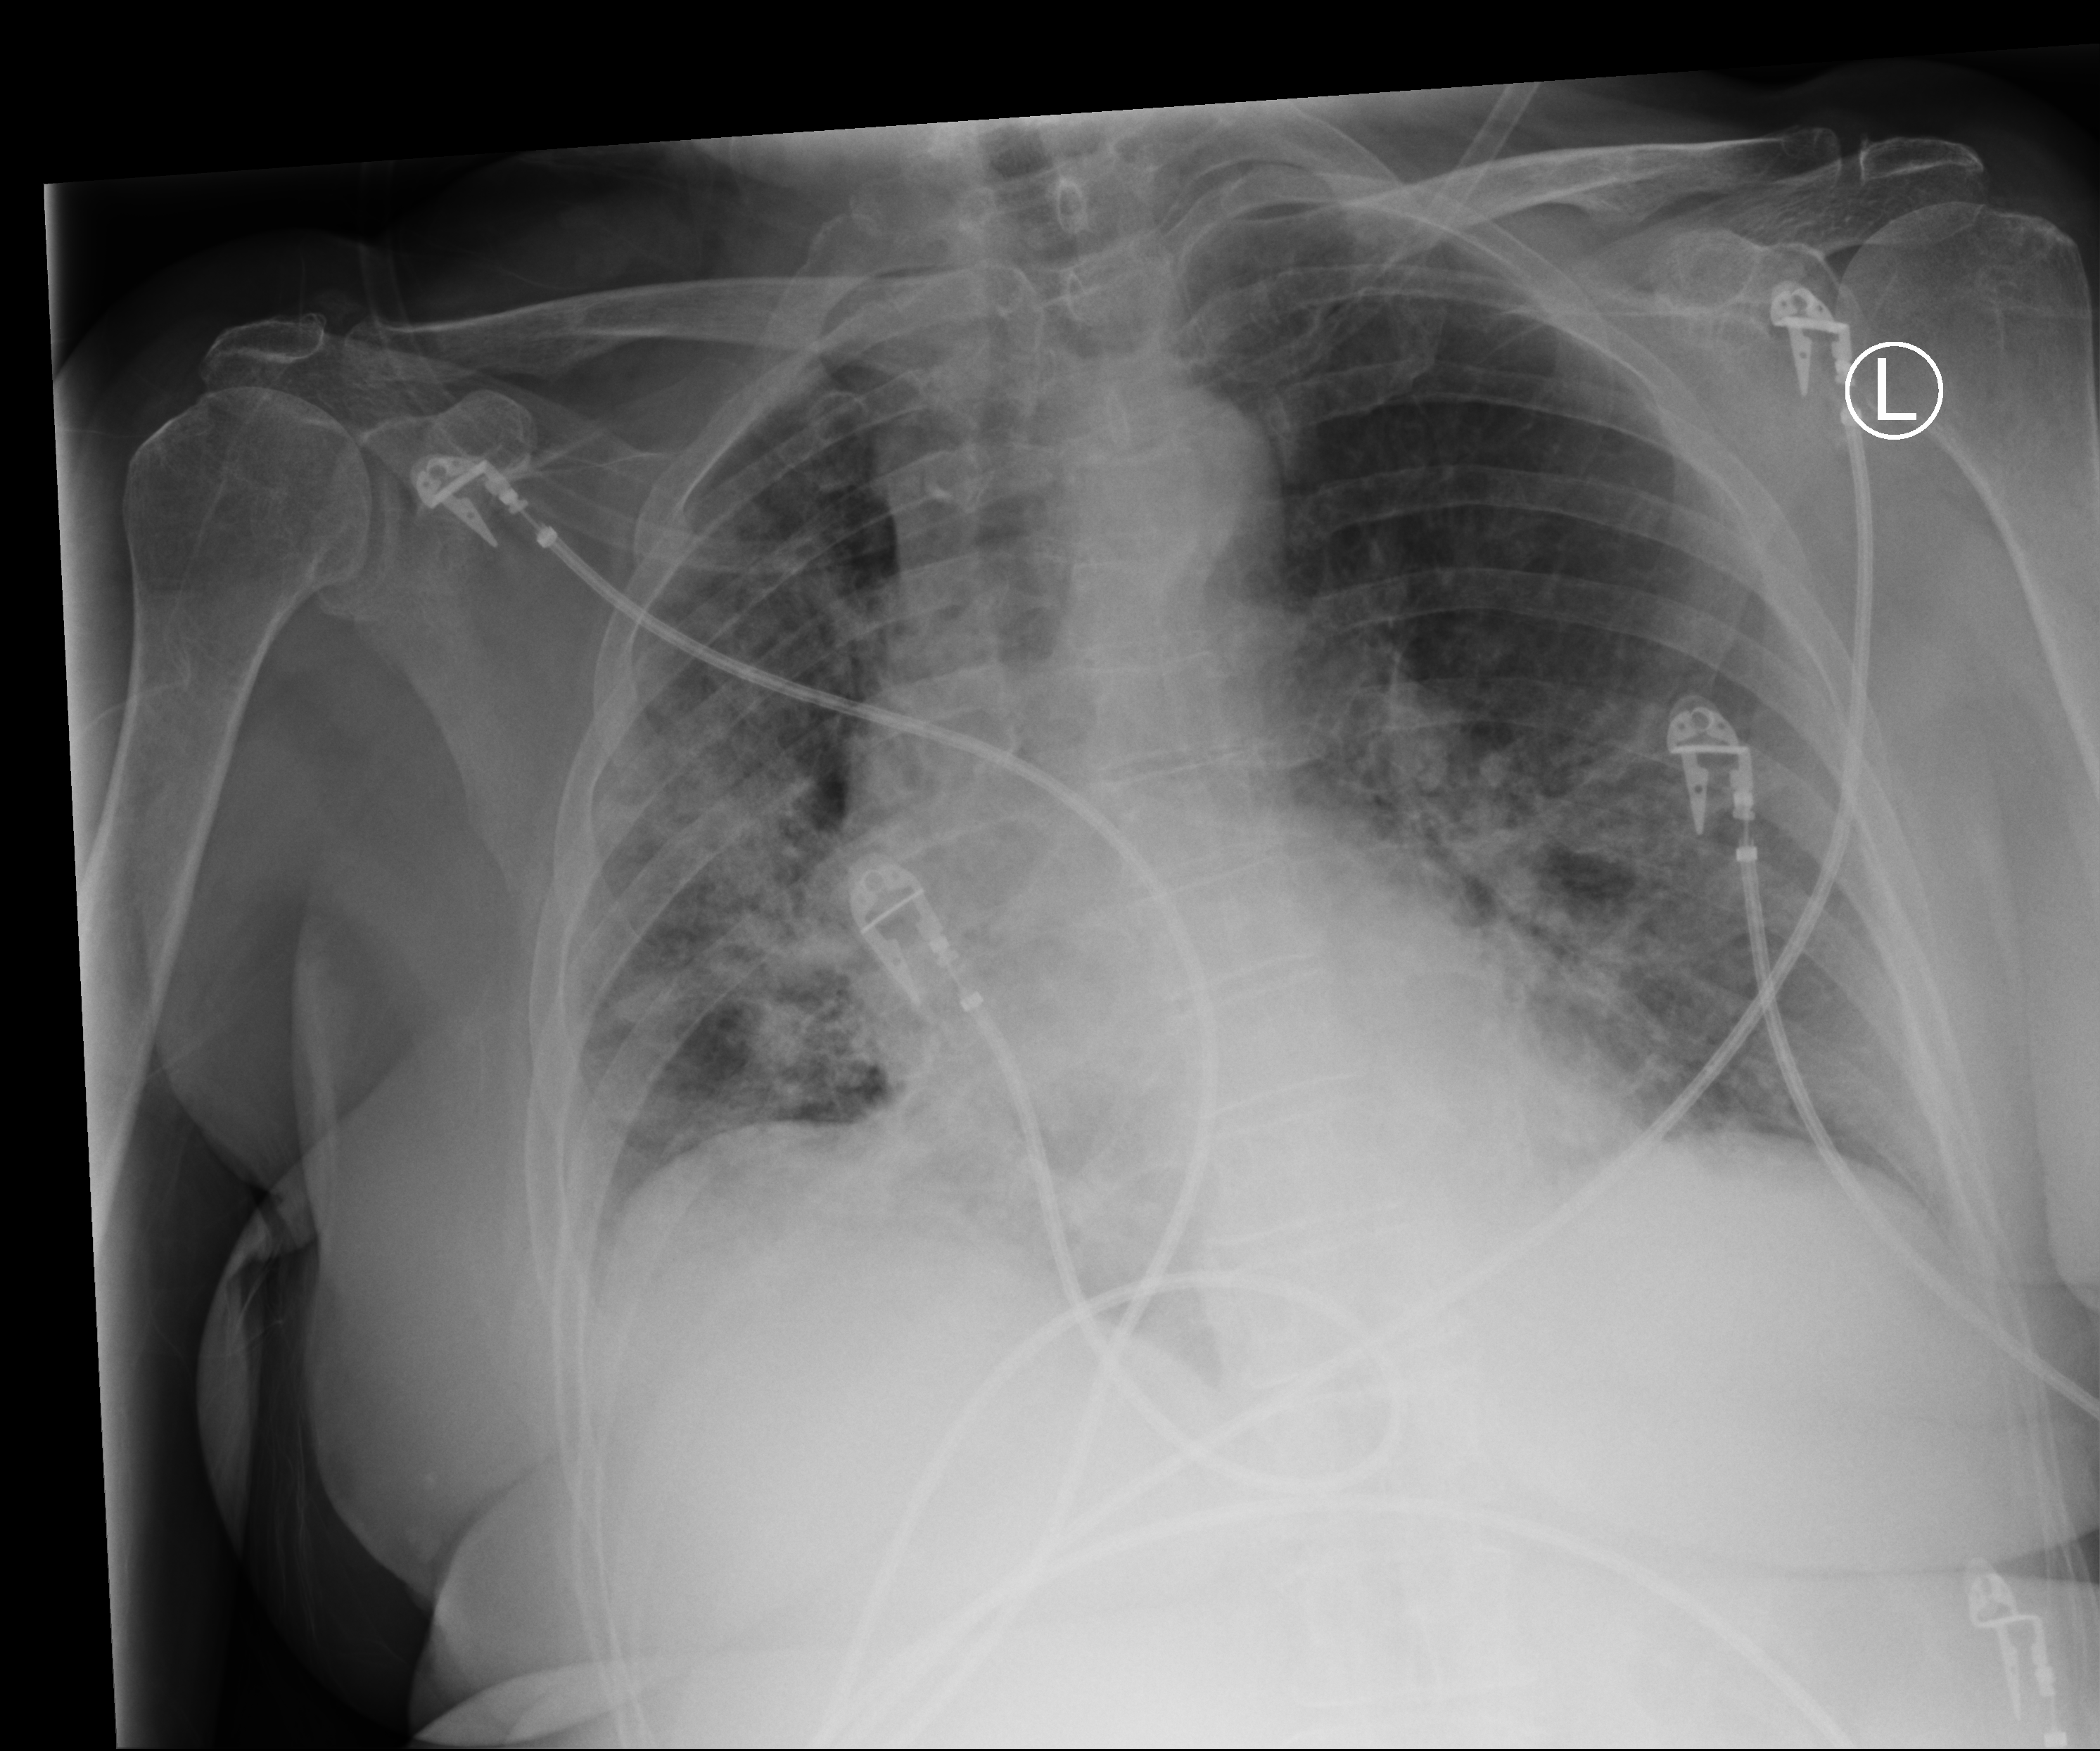
Chest X-ray (portable), anteroposterior (AP) projection. Patient hospitalised with COVID-19; female, aged 75–90 years.
Admission-level facts for this patient (not findings on this image; timing relative to this image not recorded):
- length of hospital stay: 4 days
- admitted to intensive care during this hospital stay: no
- mechanically ventilated during this hospital stay: no